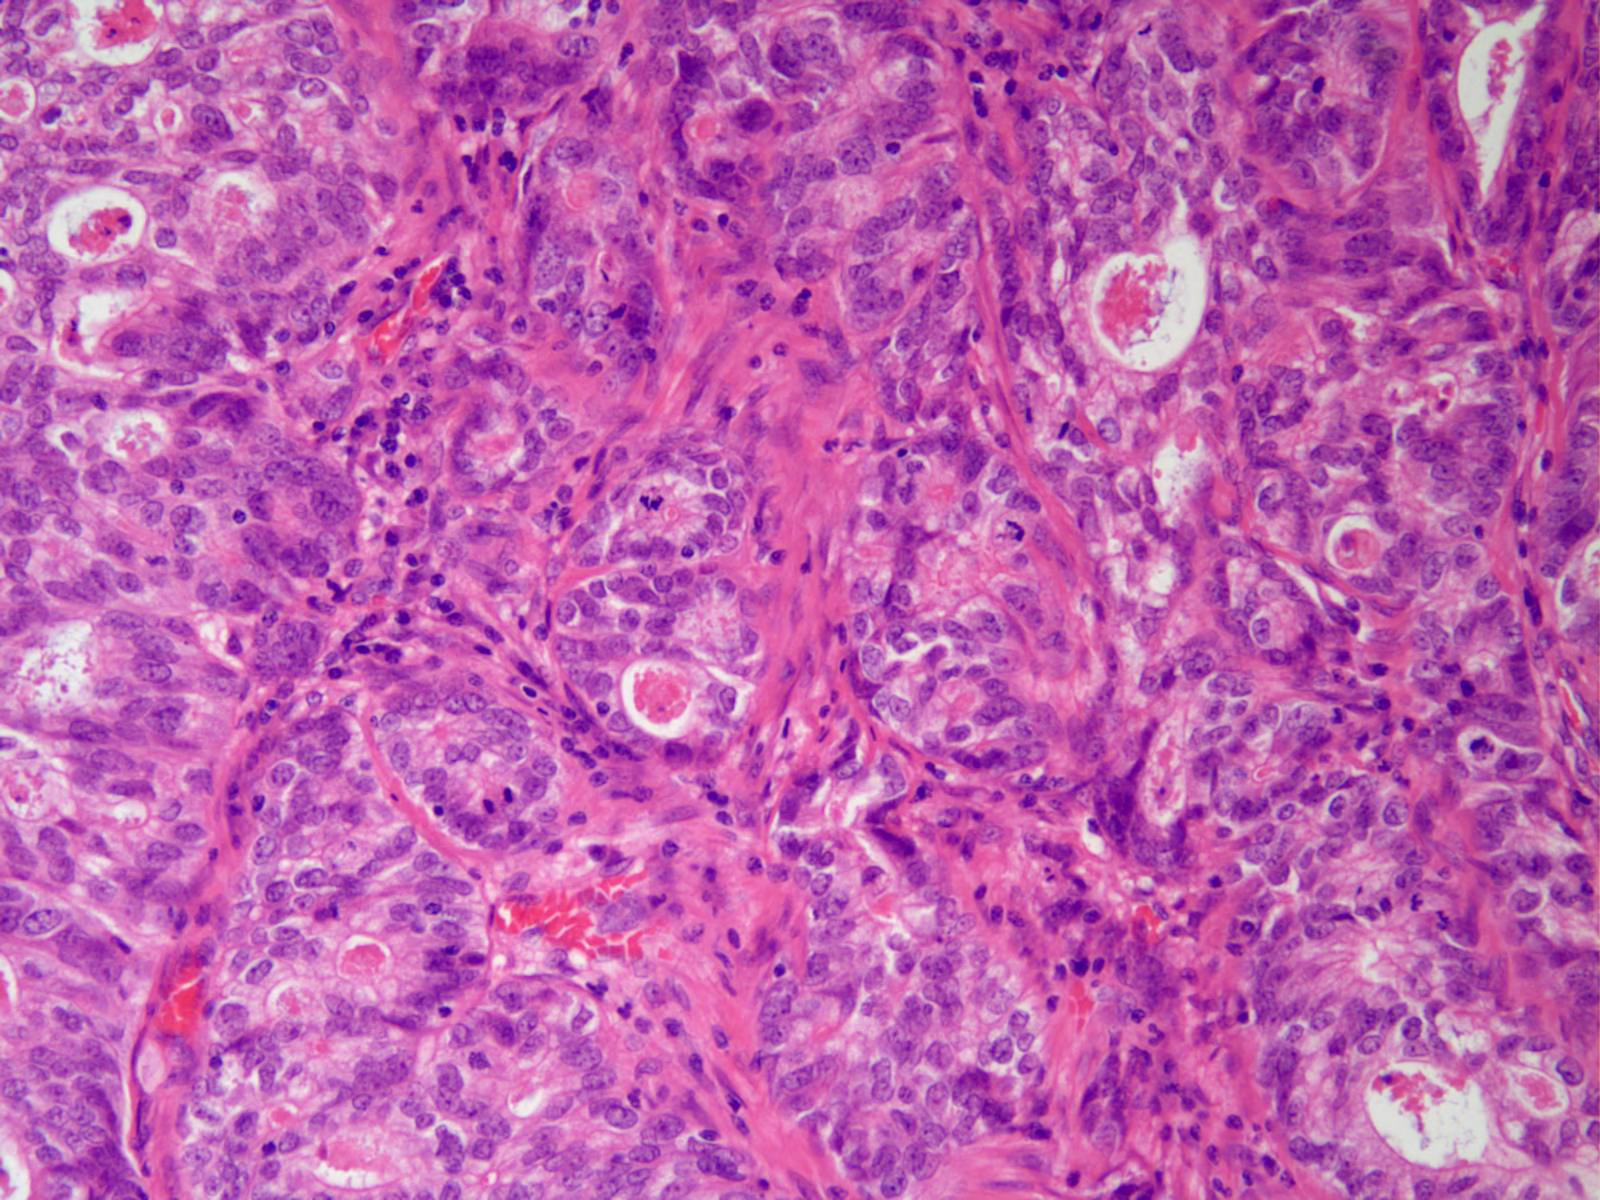
Single-field Hematoxylin and eosin (H&E) stained photomicrograph — covering about 0.8 x 0.6 mm, formalin-fixed paraffin-embedded (FFPE) diagnostic section, stomach, primary tumour sample. Patient: male, age at initial diagnosis 58 years. Histologic grade: G2 (moderately differentiated).
* diagnosis: Adenocarcinoma, NOS